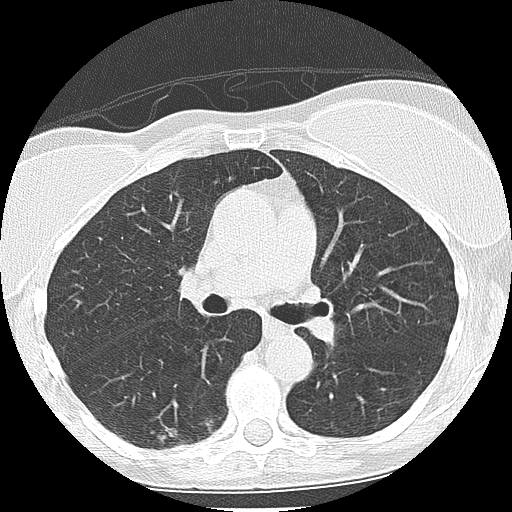
Low-dose screening chest CT, one axial slice; slice 126 of 225 in the series (ordered by position); reconstruction kernel LUNG; 120 kVp; lung window (W 1500 / L -600 HU); 2.5 mm slice thickness; 512 × 512 image matrix.
Structures marked on this image (outlined manually by an expert reader):
- lesion 1 (tumor, lower lobe of right lung): bounding box [x1, y1, x2, y2] px = [159, 427, 181, 447]